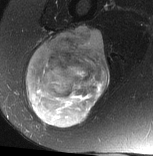
MRI of an extremity soft-tissue mass, one axial slice; position 37 of 77 along the scan axis; T2-weighted fat-saturated; MR volume resampled by the dataset authors to the PET/CT grid (not the native acquisition matrix); 3.27 mm slice thickness; 153 × 156 image matrix, field of view 149 × 152 mm. Female patient. Case-level facts recorded for this patient, not image findings: histological type: synovial sarcoma; grade: intermediate; site of the primary tumour: right buttock.
Outlined on this slice (expert contour drawn on MRI and transferred to this co-registered scan by the dataset authors):
- gross tumour volume including surrounding oedema: bounding box [x1, y1, x2, y2] px = [26, 27, 111, 128]
- gross tumour volume (mass): [26, 27, 111, 128]